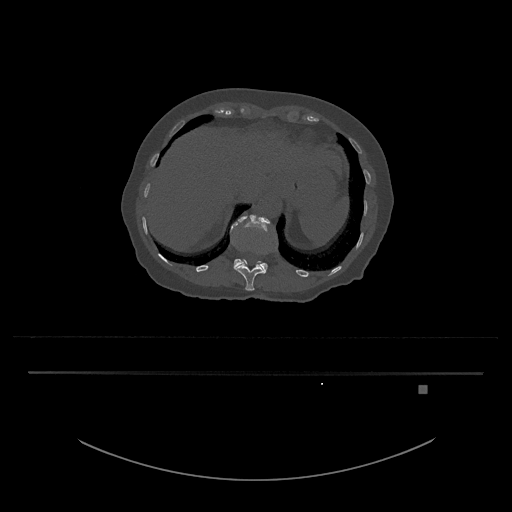
CT including the spine, one axial slice; position 589 of 797 along the scan axis; reconstruction kernel Br40s/3; bone window (W 1800 / L 400 HU); 0.5 mm slice thickness; 512 × 512 image matrix, field of view 500 × 500 mm. Patient: female, 57 years. Case-level facts recorded for this patient, not image findings: primary cancer: cervical.
Structures marked on this image (semi-automatically segmented with operator editing):
- L1 vertebra: bounding box (x1, y1, x2, y2) in pixels: (230, 215, 277, 271)
- T12 vertebra: (235, 260, 266, 291)